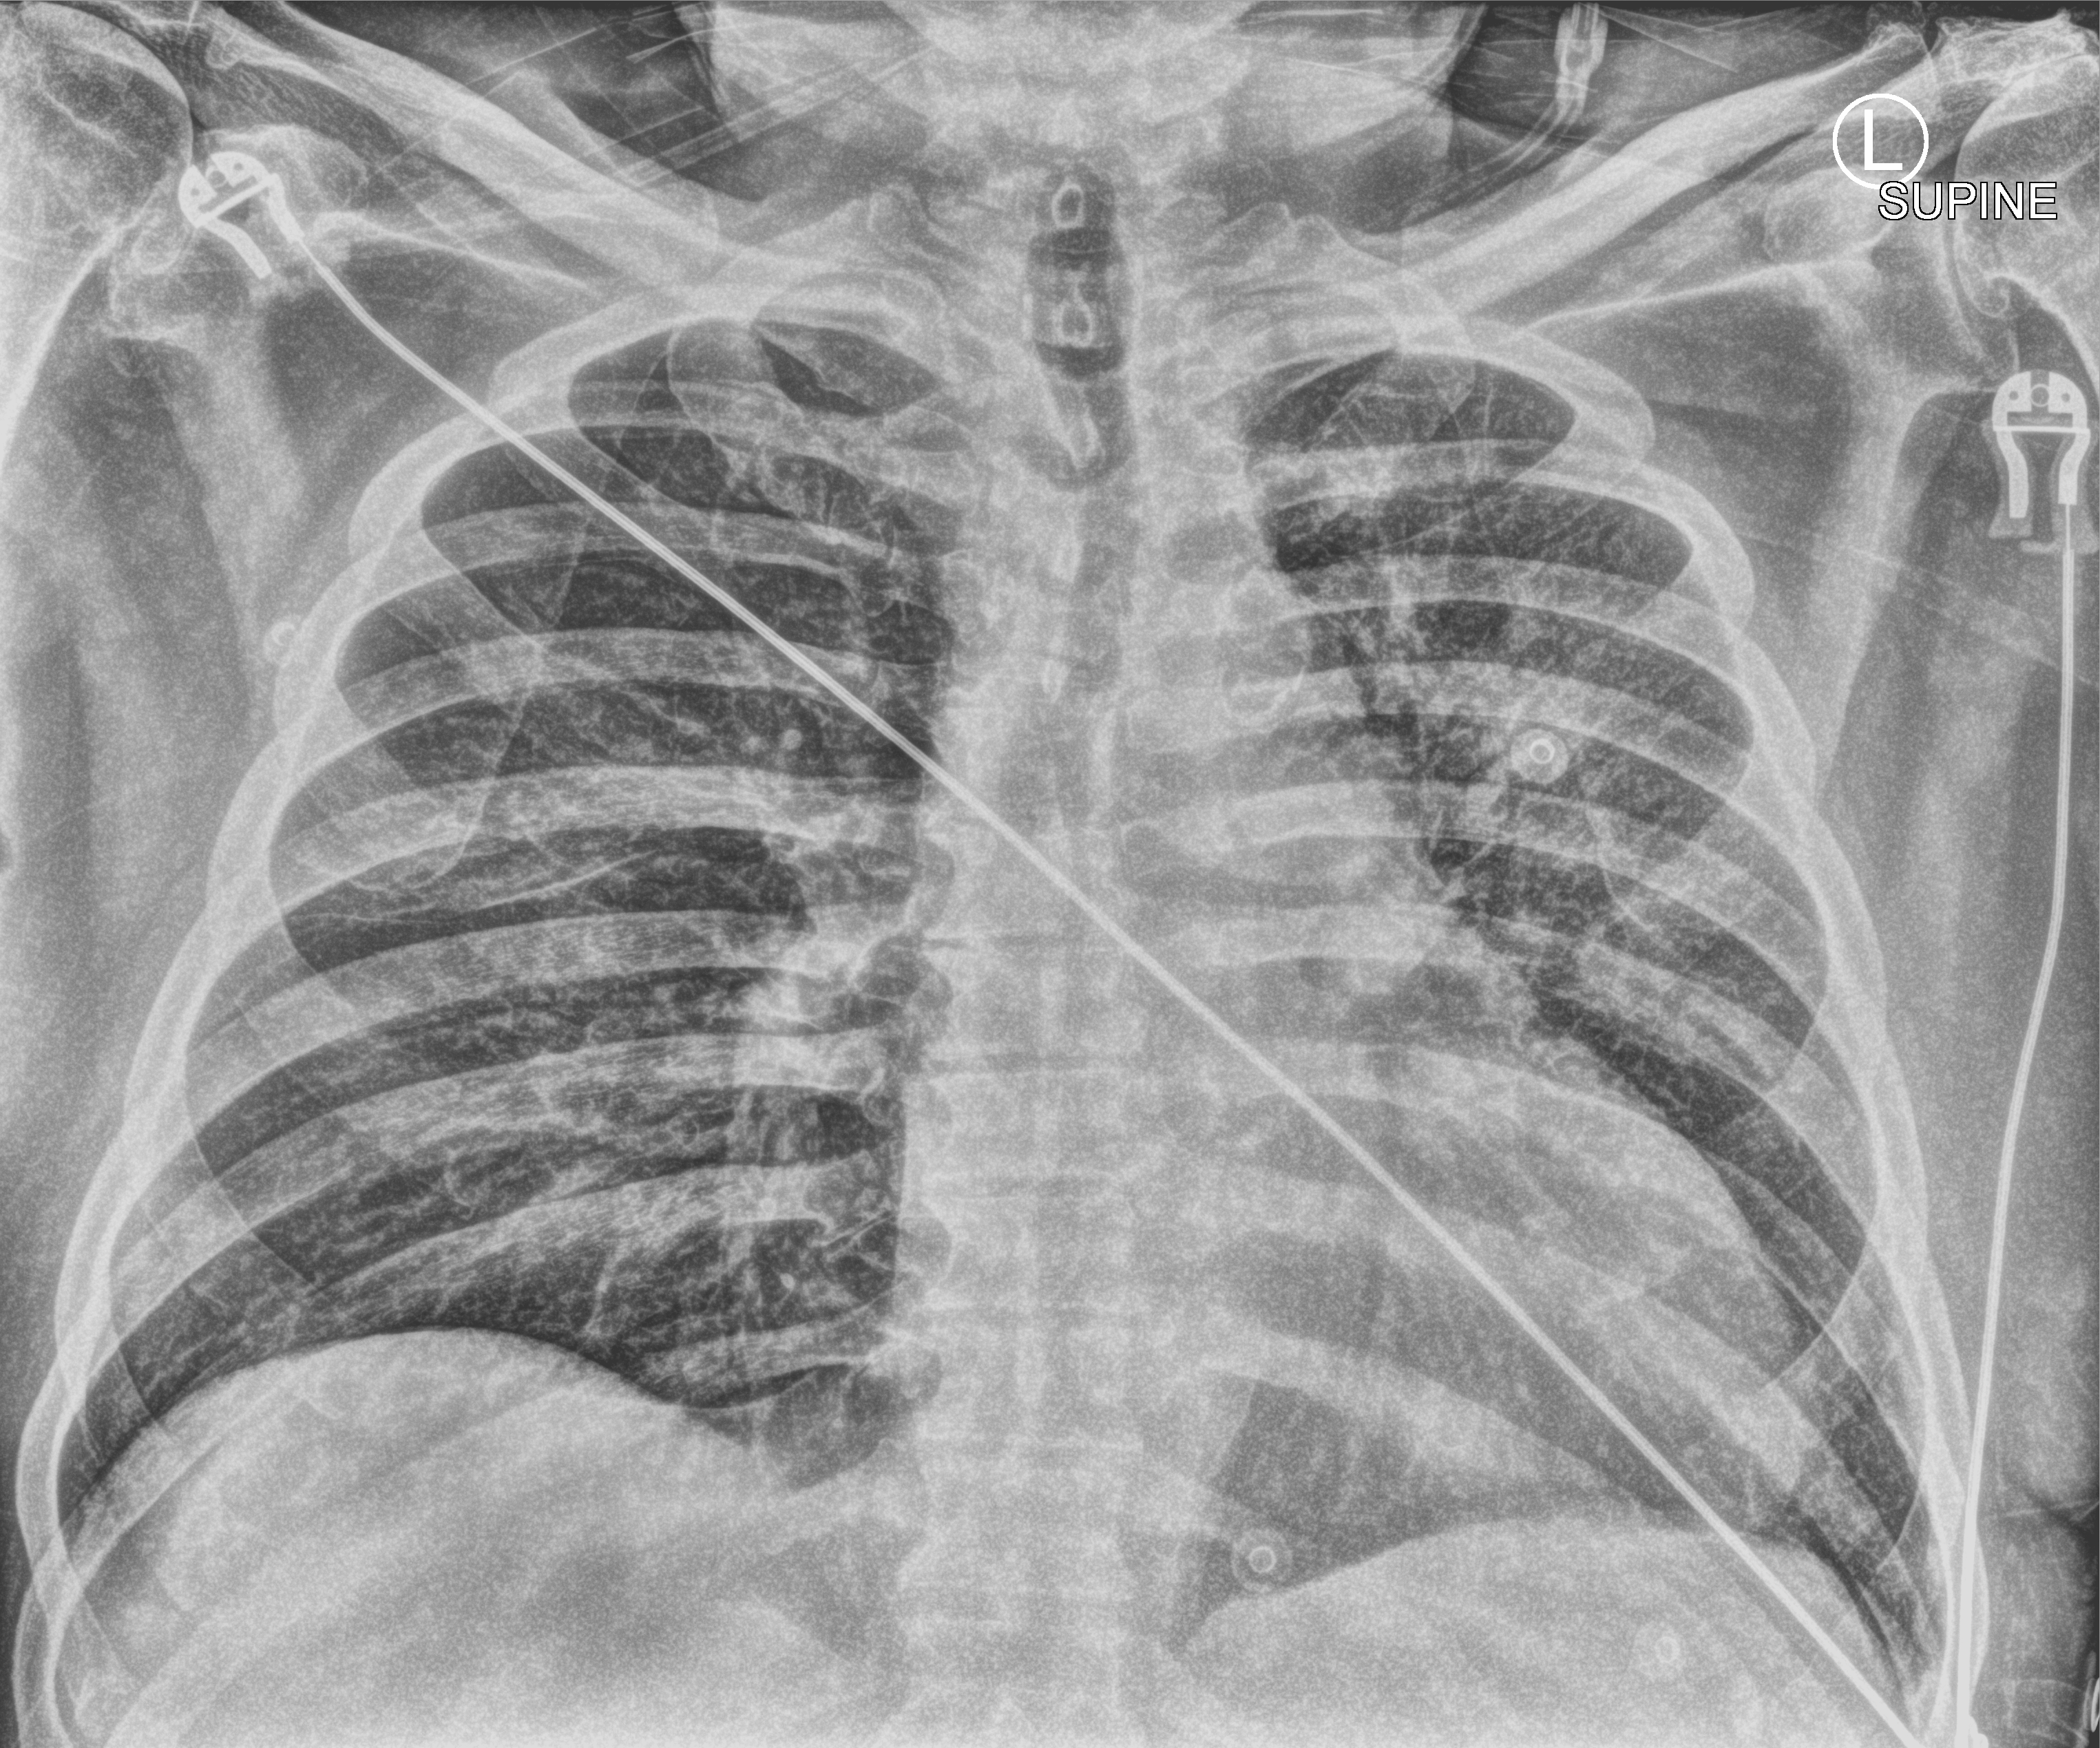
Portable chest radiograph, anteroposterior (AP) projection. Male patient hospitalised with COVID-19, age 60–74 years.
From the hospital-stay record, not from the radiograph (when in the stay this image was taken is not recorded): admitted to intensive care during this hospital stay: yes.